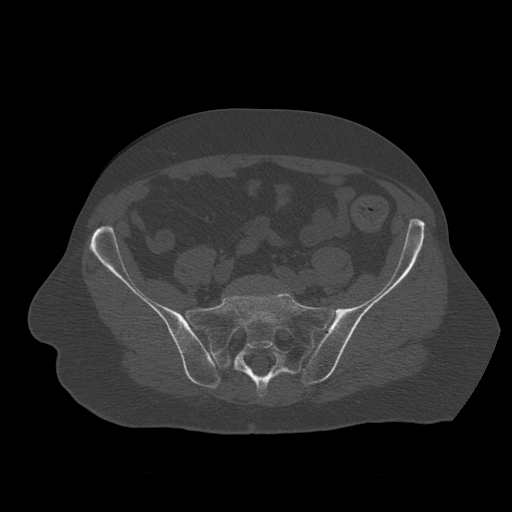
CT including the spine, one axial slice; slice 232 of 450 in the series (ordered by position); reconstruction kernel STANDARD; 120 kVp; bone window (W 1800 / L 400 HU); 512 × 512 image matrix, field of view 405 × 405 mm. Patient age 75 years. From the clinical record (not read from this slice): primary cancer: prostate.
Outlined on this slice (semi-automatic segmentation, software-assisted and operator-edited):
- L5 vertebra: bounding box <240,276,286,292> (left, top, right, bottom; pixels)